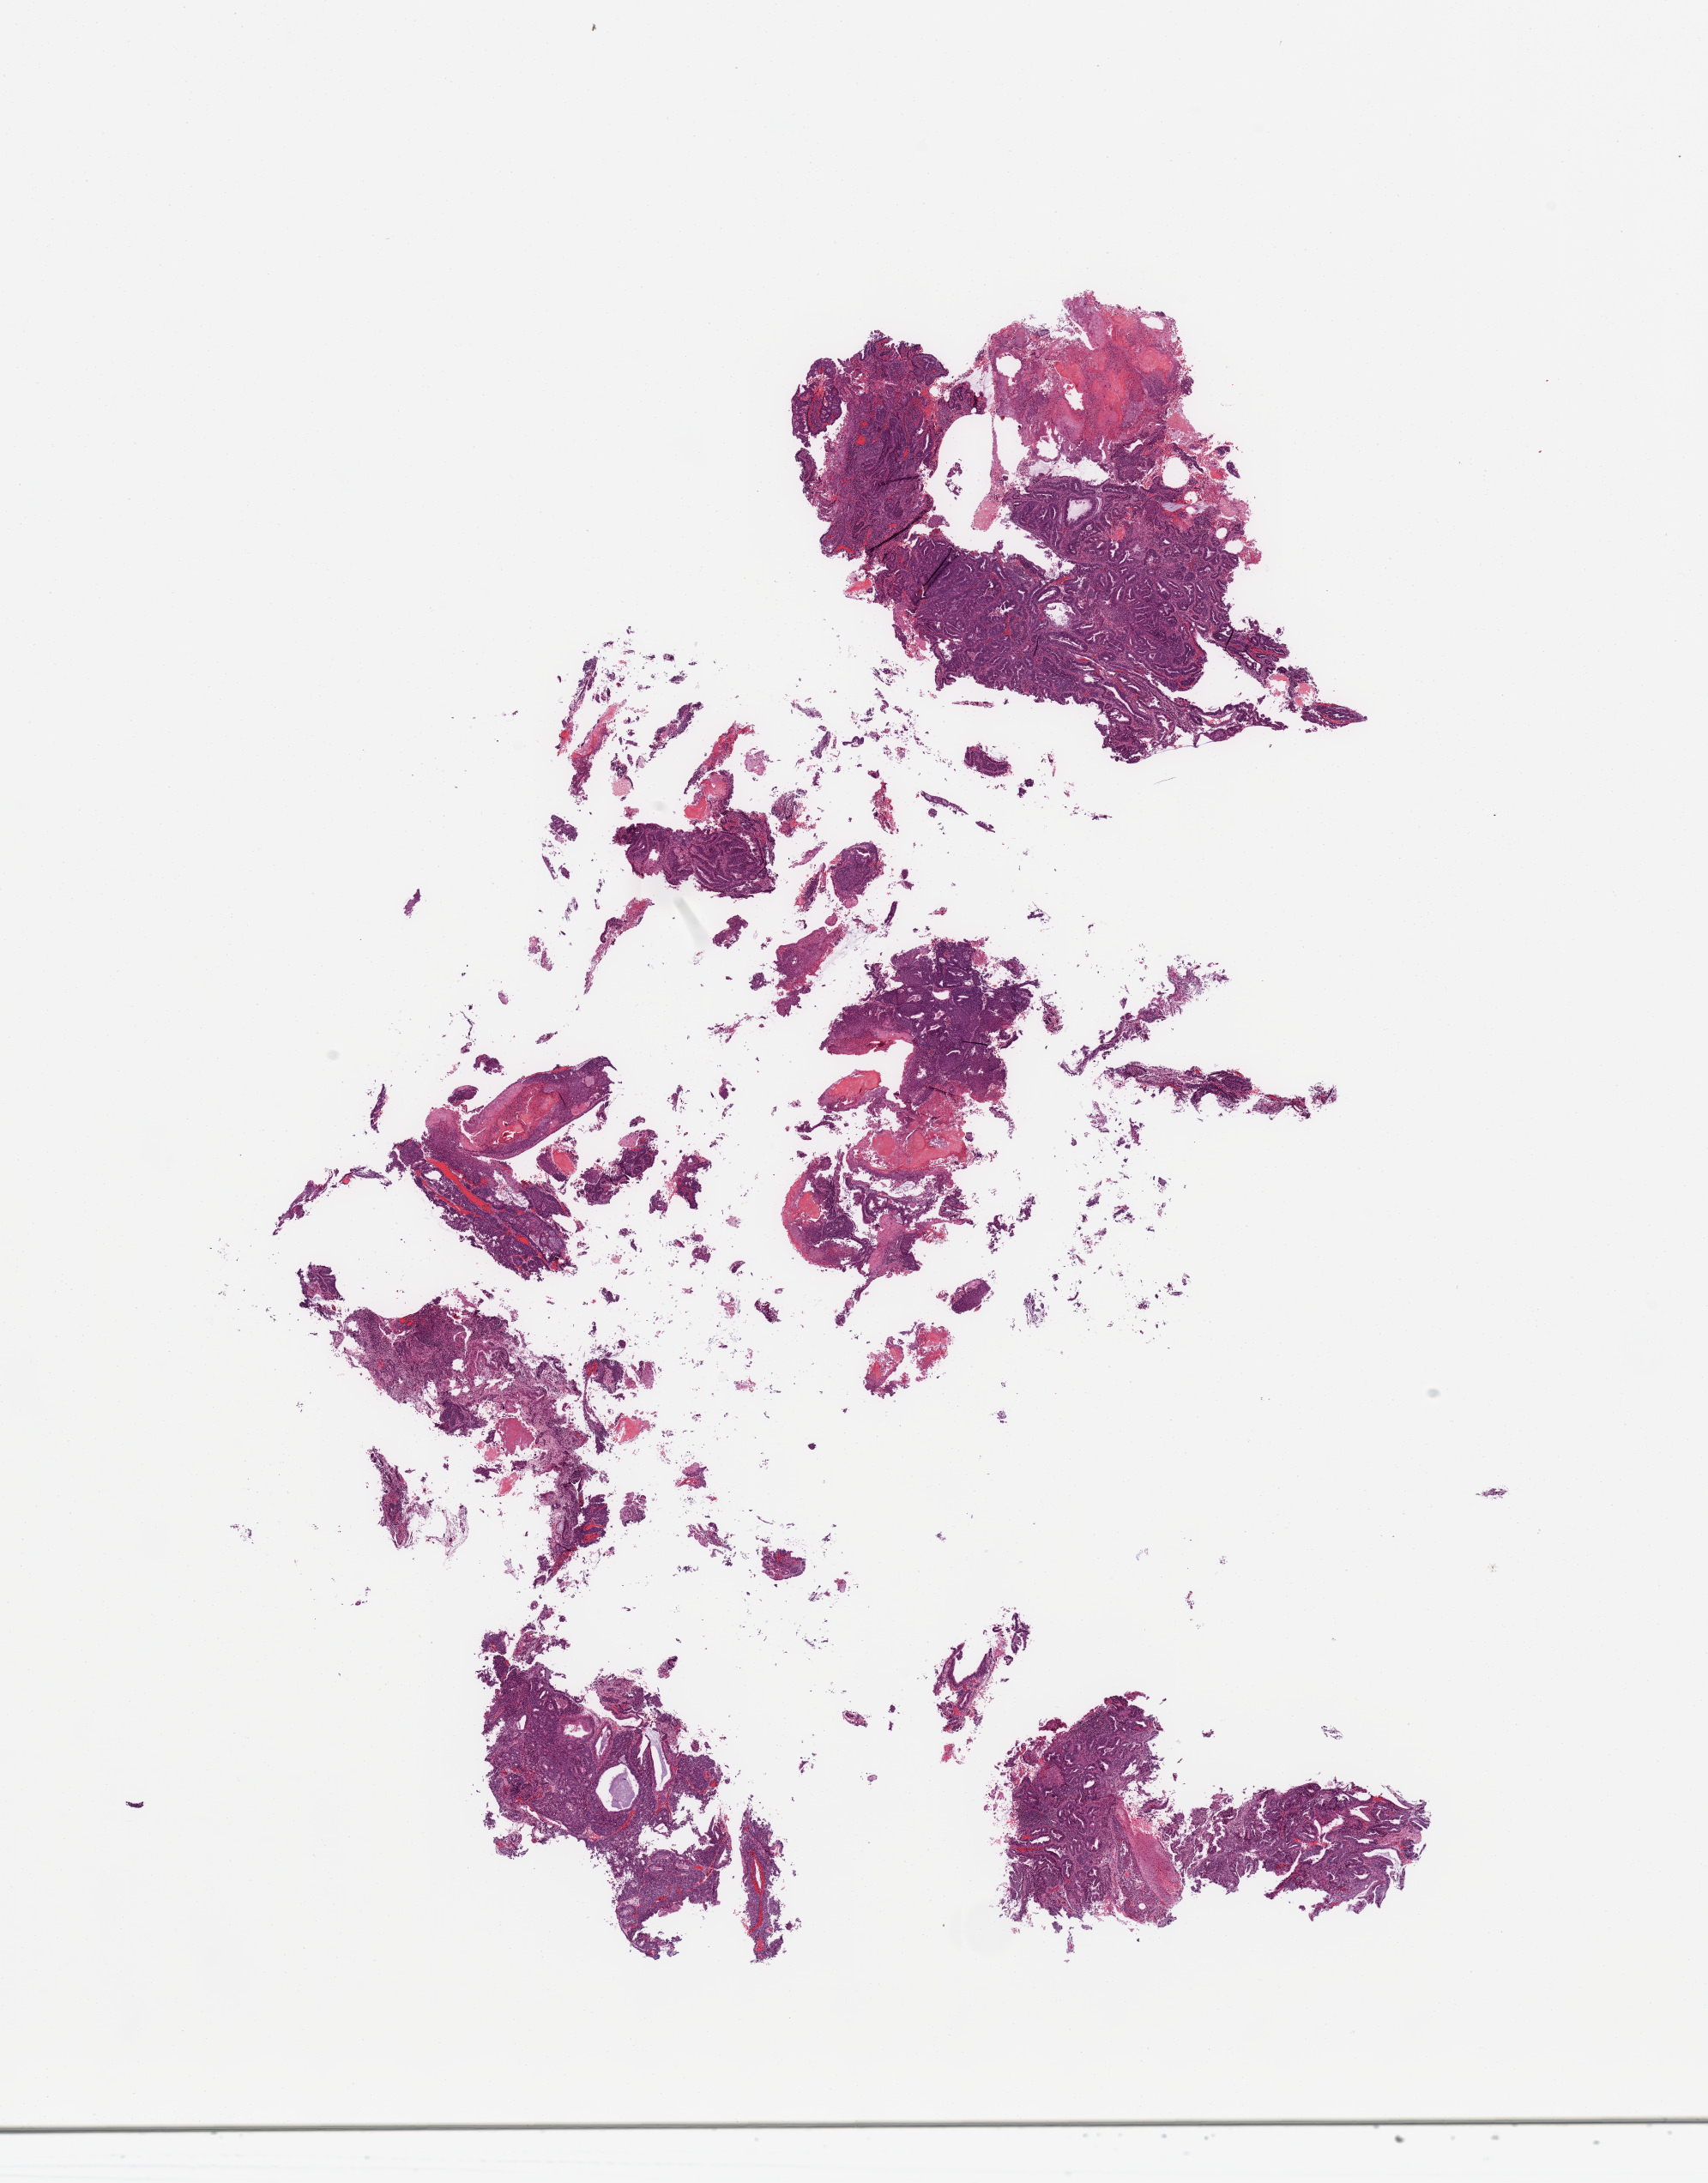
Digitized H&E-stained tissue section (whole slide) — whole scanned area (about 15.8 x 20.1 mm, from a 20x scan) shown as a low-resolution overview, tumour tissue sample, sampled site: uterus. 73-year-old female patient.
Histologic diagnosis: Endometrioid adenocarcinoma, NOS.